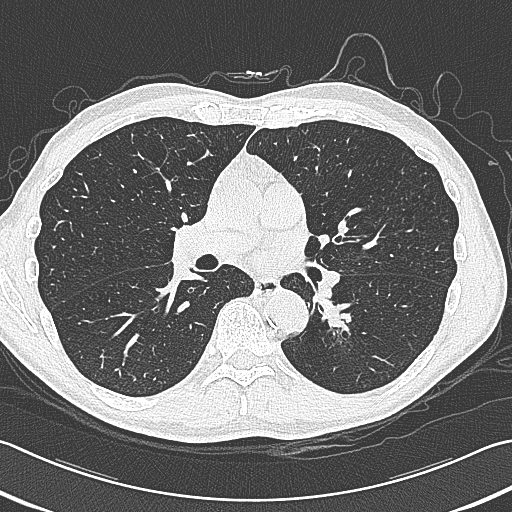
Chest CT (low-dose screening protocol), one axial image, baseline screening round, lung window (W 1500 / L -600 HU), lung (sharp) reconstruction kernel (B80f), slice 163 of 354 in the series, 512 × 512 image matrix. Male, age 59 years at enrolment.
Expert-annotated lung lesion, box from (x=314, y=292) to (x=375, y=352) px. Reader record for this screening exam (exam-level; its link to the box is not recorded): non-calcified nodule or mass ≥4 mm, left lower lobe, 15 × 15 mm, smooth margins, soft tissue attenuation. Official screen result: positive, change unspecified: nodule(s) >= 4 mm or enlarging nodule(s), mass(es), or other non-specific abnormalities suspicious for lung cancer. Lung cancer was diagnosed 17 days after this screen: squamous cell carcinoma, large cell, nonkeratinizing, NOS, left lower lobe, poorly differentiated (G3), stage IB (AJCC 6th edition), 31 mm at pathology.